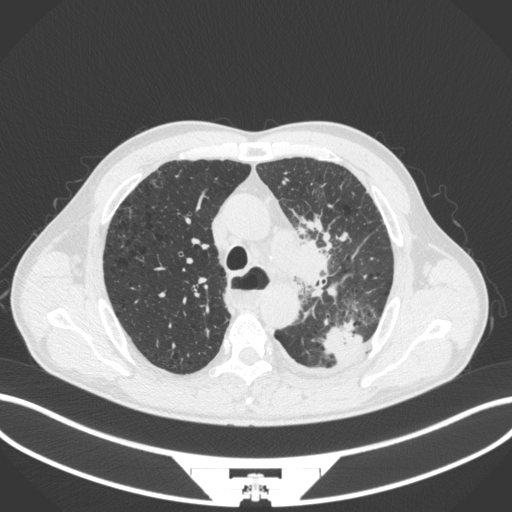
Chest CT, one axial slice. Slice 279 of 411 in the series (ordered by position). Lung window (W 1500 / L -600 HU). 512 × 512 image matrix, field of view 400 × 400 mm. Patient: male, 57 years. Case-level facts recorded for this patient, not image findings: clinical TNM (as recorded): T2a N1 M0.
Annotated regions visible in this slice (bounding box drawn by a radiologist):
- lung tumour (recorded histology: squamous cell carcinoma): box from (x=269, y=232) to (x=337, y=285) px